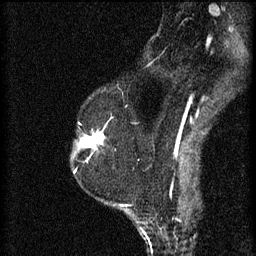
Breast MRI (dynamic contrast-enhanced), one sagittal slice. Position 45 of 60 along the scan axis. 3 images stored at this slice position (order not interpretable as contrast timing). 1.5 T. TE 4.2 ms, TR 8.2 ms. 256 × 256 image matrix, field of view 180 × 180 mm. Patient: female, 60 years.
Annotated regions visible in this slice (semi-automatically segmented with operator editing):
- analysis volume of interest (the breast-tissue region the enhancement analysis was run in; not a lesion): bounding box <74,124,105,159> (left, top, right, bottom; pixels)
- tumour enhancement mask (voxels above the 70 % enhancement threshold inside the analysis volume of interest): <80,132,105,149>